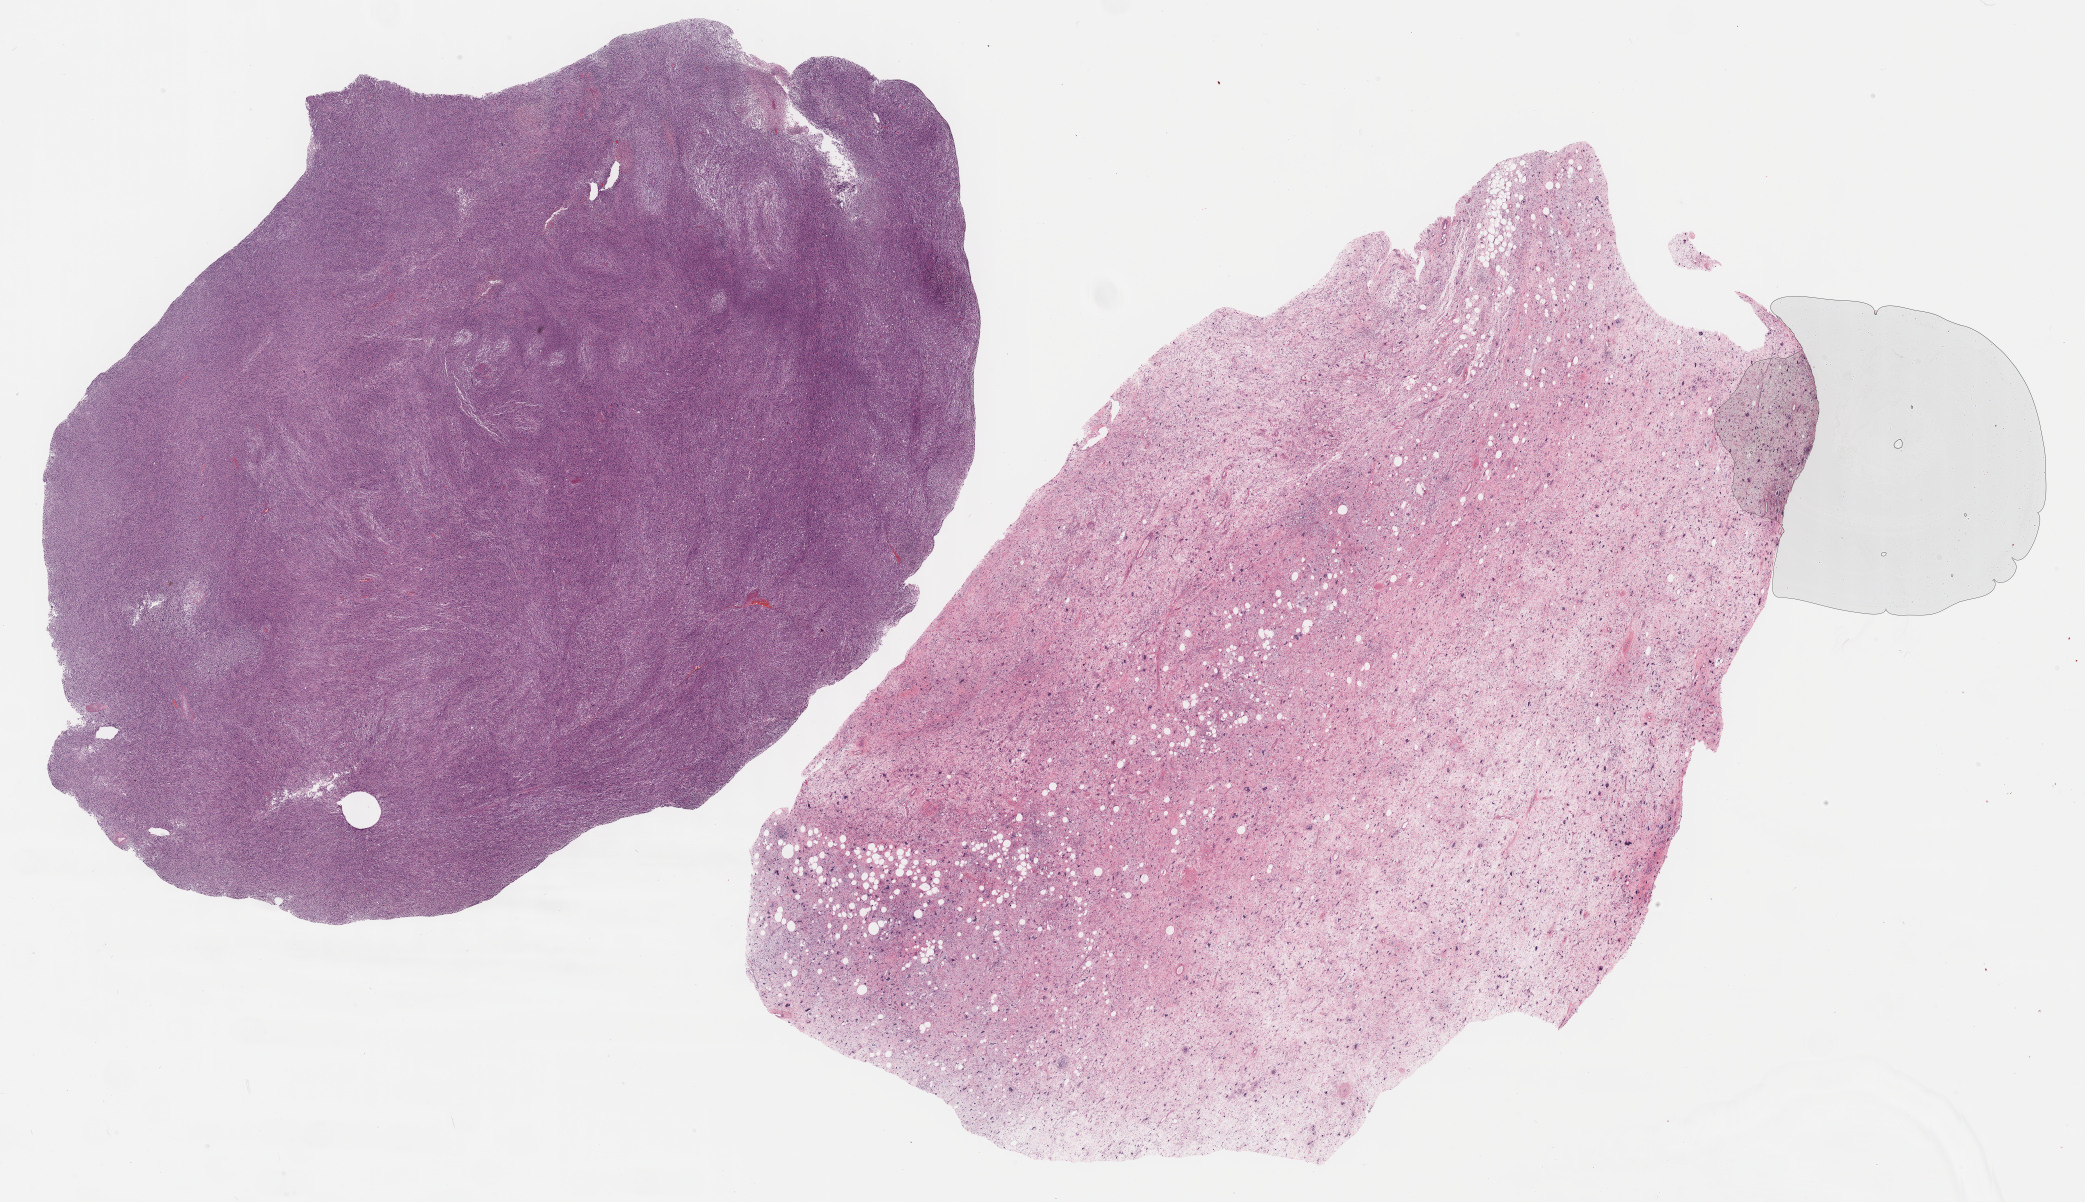
H&E-stained whole-slide image, low-resolution overview of the scanned area, about 33.7 x 19.4 mm (slide scanned at 40x); FFPE section; sample: primary tumour, retroperitoneum and peritoneum. Patient: female, age at initial diagnosis 40 years.
Diagnosis: Dedifferentiated liposarcoma.